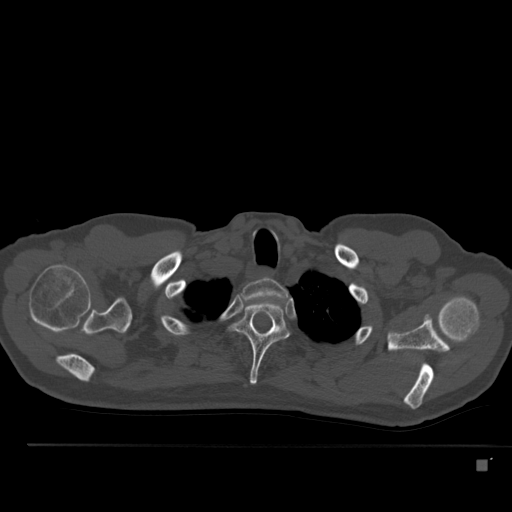
CT including the spine, one axial slice. Reconstruction kernel Br40s. 120 kVp. Bone window (W 1800 / L 400 HU). 1.5 mm slice thickness. 512 × 512 image matrix, field of view 408 × 408 mm. Patient: male, 70 years. From the clinical record (not read from this slice): primary cancer: renal; vertebrae with lytic lesions (as recorded): T4, T6, T10, T12, L3, L4, L5.
Annotated regions visible in this slice (semi-automatically segmented with operator editing):
- T1 vertebra: bounding box (x1, y1, x2, y2) in pixels: (242, 278, 288, 300)
- T2 vertebra: (230, 300, 289, 385)